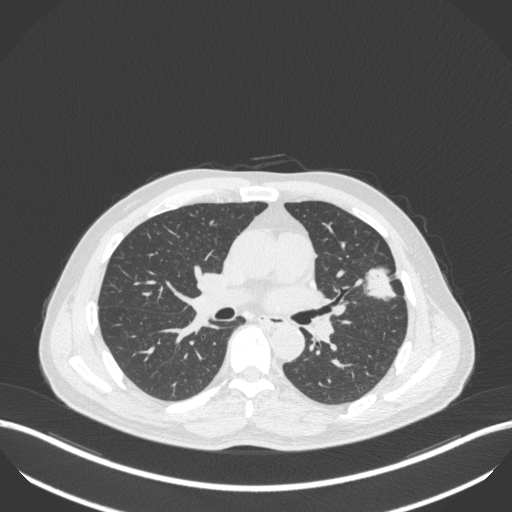
Chest CT, one axial slice. Lung window (W 1500 / L -600 HU). 1 mm slice thickness. 512 × 512 image matrix, field of view 400 × 400 mm. Patient: male, 55 years. From the clinical record (not read from this slice): clinical TNM (as recorded): T1c N0 M0; histopathological grade: G2-3.
Outlined on this slice (rectangle marked by the reading radiologist):
- lung tumour (recorded histology: adenocarcinoma): bounding box [x1, y1, x2, y2] px = [362, 262, 397, 305]